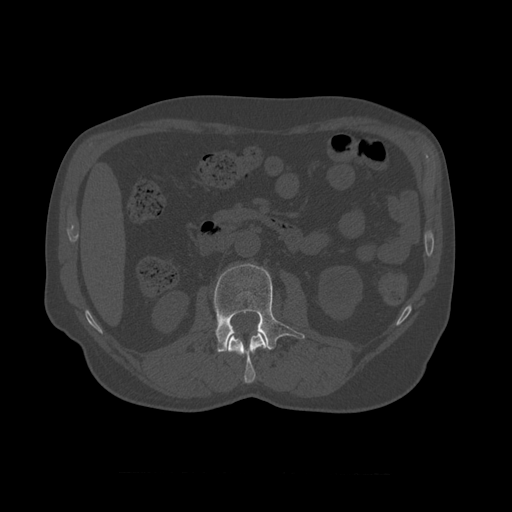
CT including the spine, one axial slice; position 337 of 450 along the scan axis; bone window (W 1800 / L 400 HU); 1.25 mm slice thickness; 512 × 512 image matrix, field of view 405 × 405 mm. Patient age 75 years. Case-level facts recorded for this patient, not image findings: primary cancer: prostate.
Outlined on this slice (semi-automatically segmented with operator editing):
- L1 vertebra: bounding box [x1, y1, x2, y2] px = [226, 330, 267, 384]
- L2 vertebra: [214, 264, 305, 353]